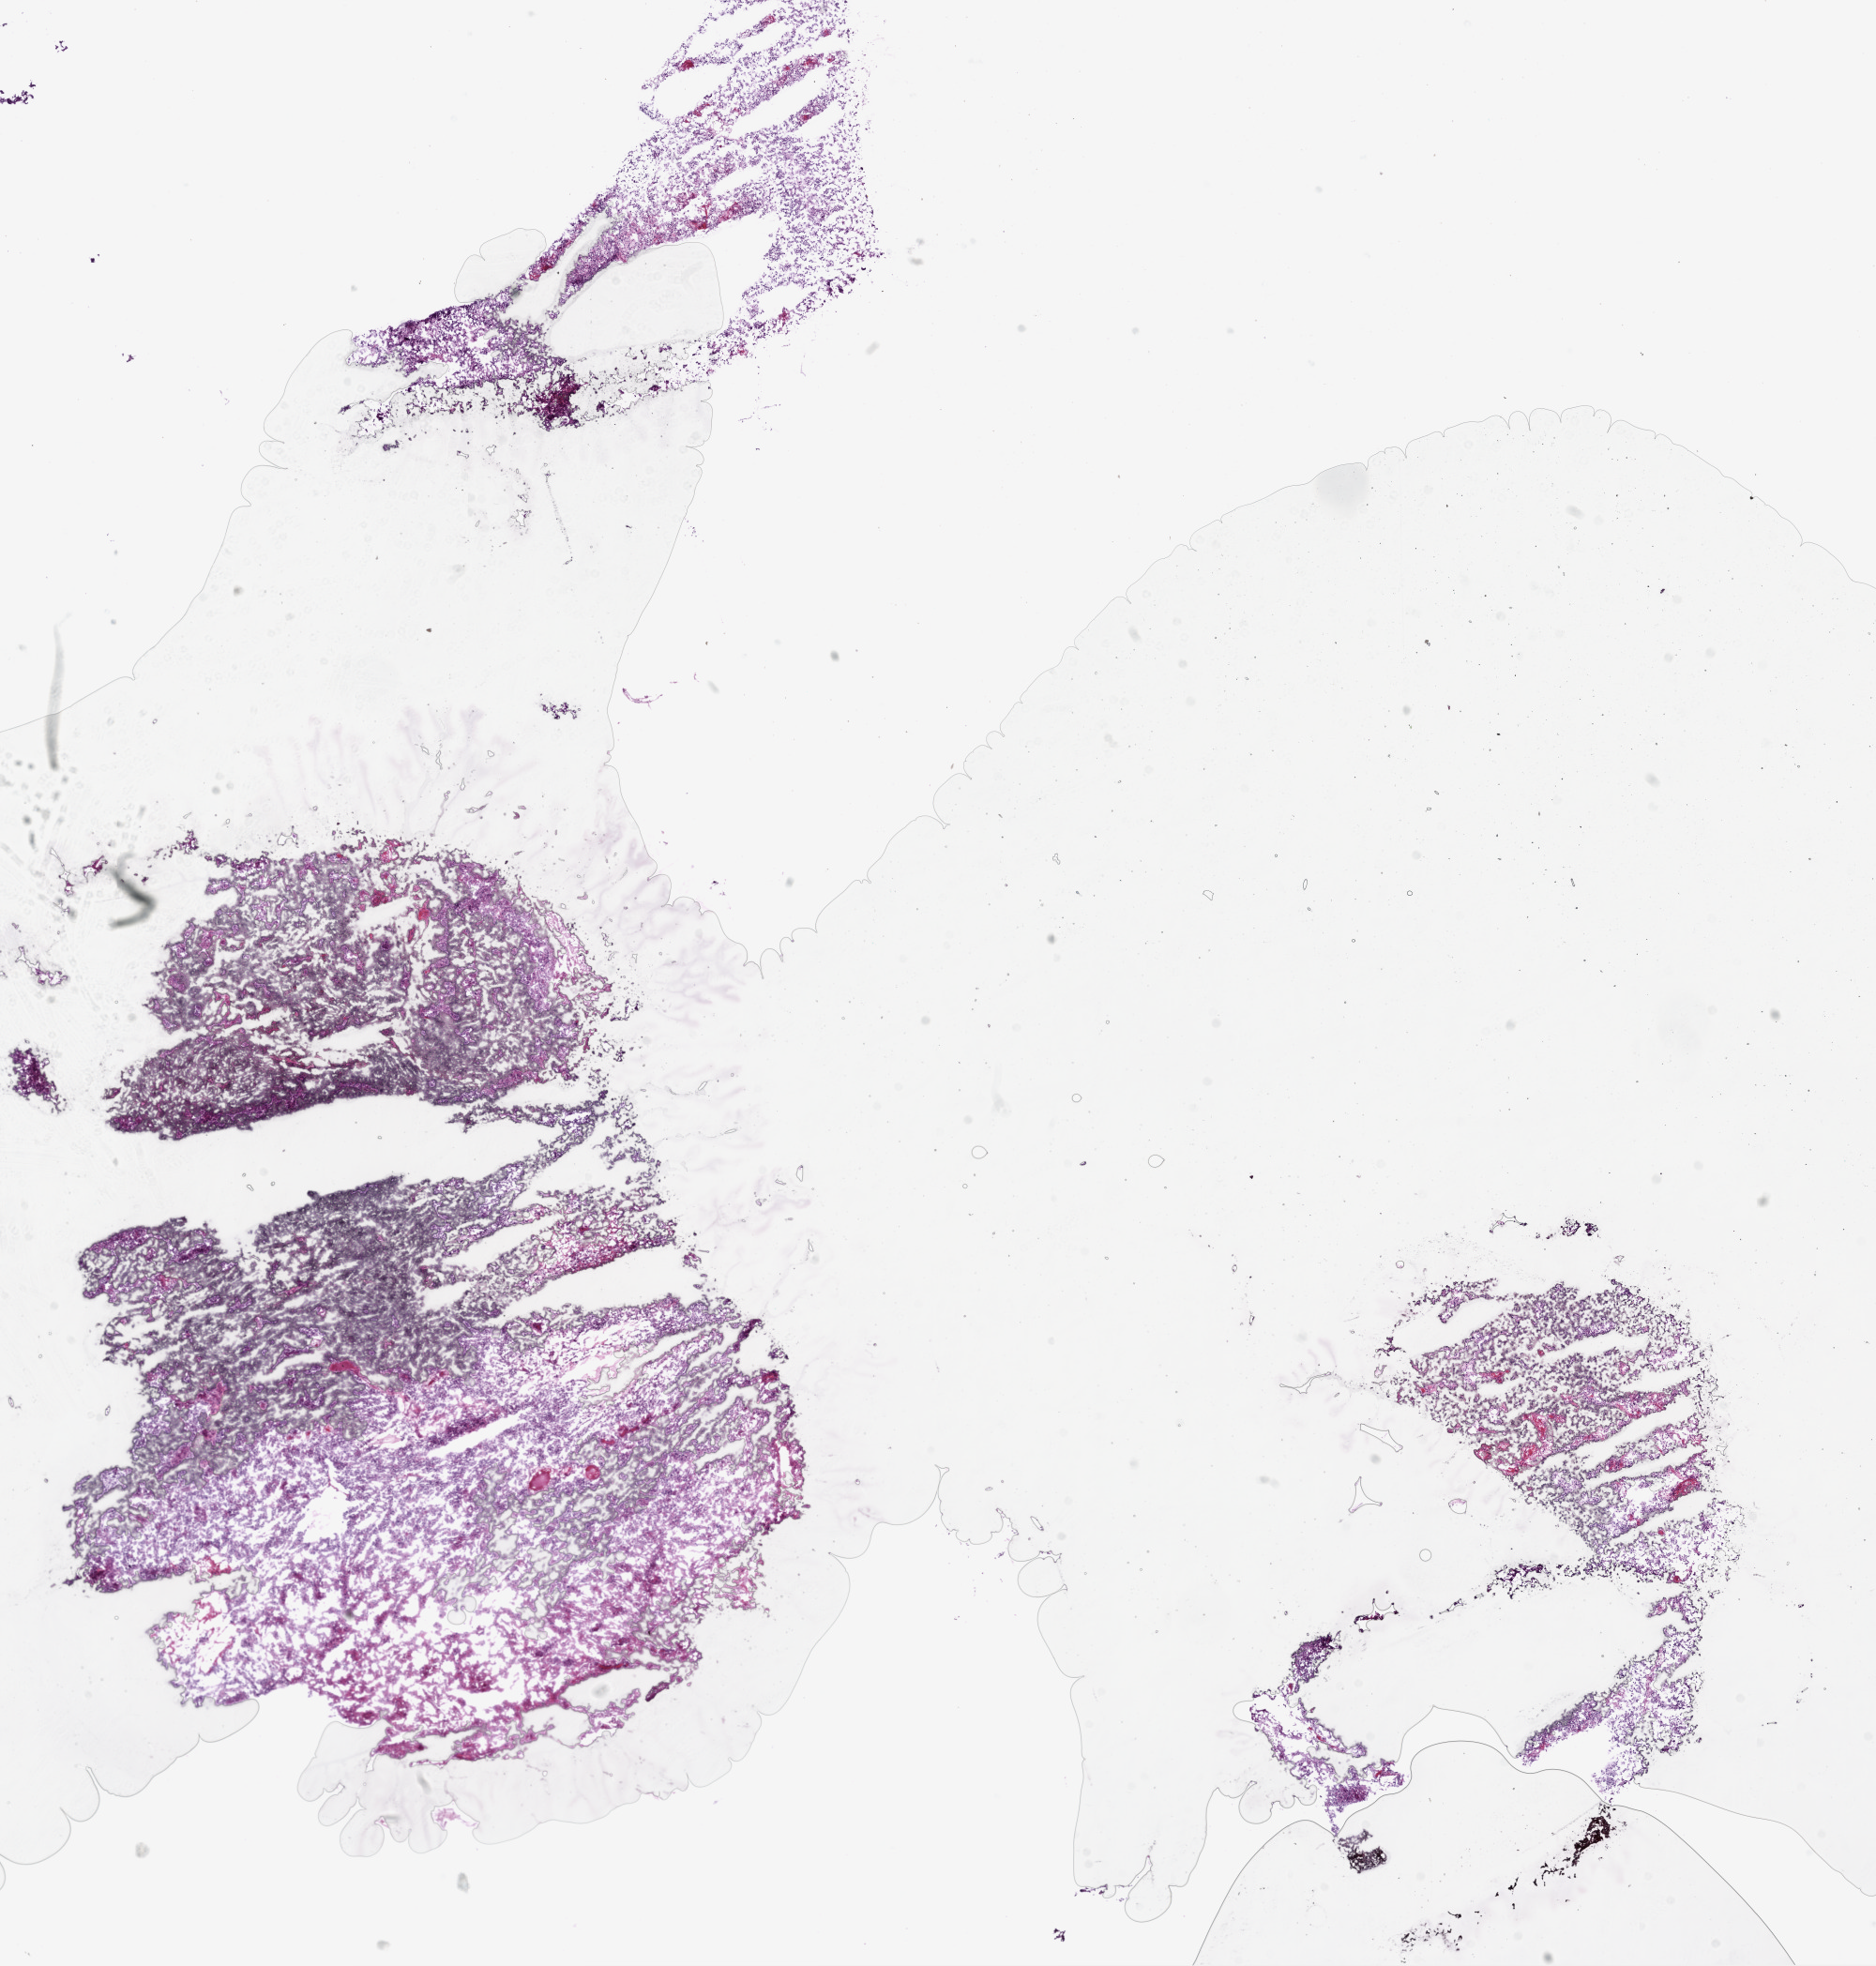
Whole-slide histology image, H&E — whole scanned area (about 16.0 x 16.8 mm) shown as a low-resolution overview. Frozen section from the bottom of the tissue portion. Brain, primary tumour sample. Male, age 76 years at initial diagnosis. Slide review estimates, as recorded: tumour cells 95%, tumour nuclei 80%.
Diagnosis: Glioblastoma.